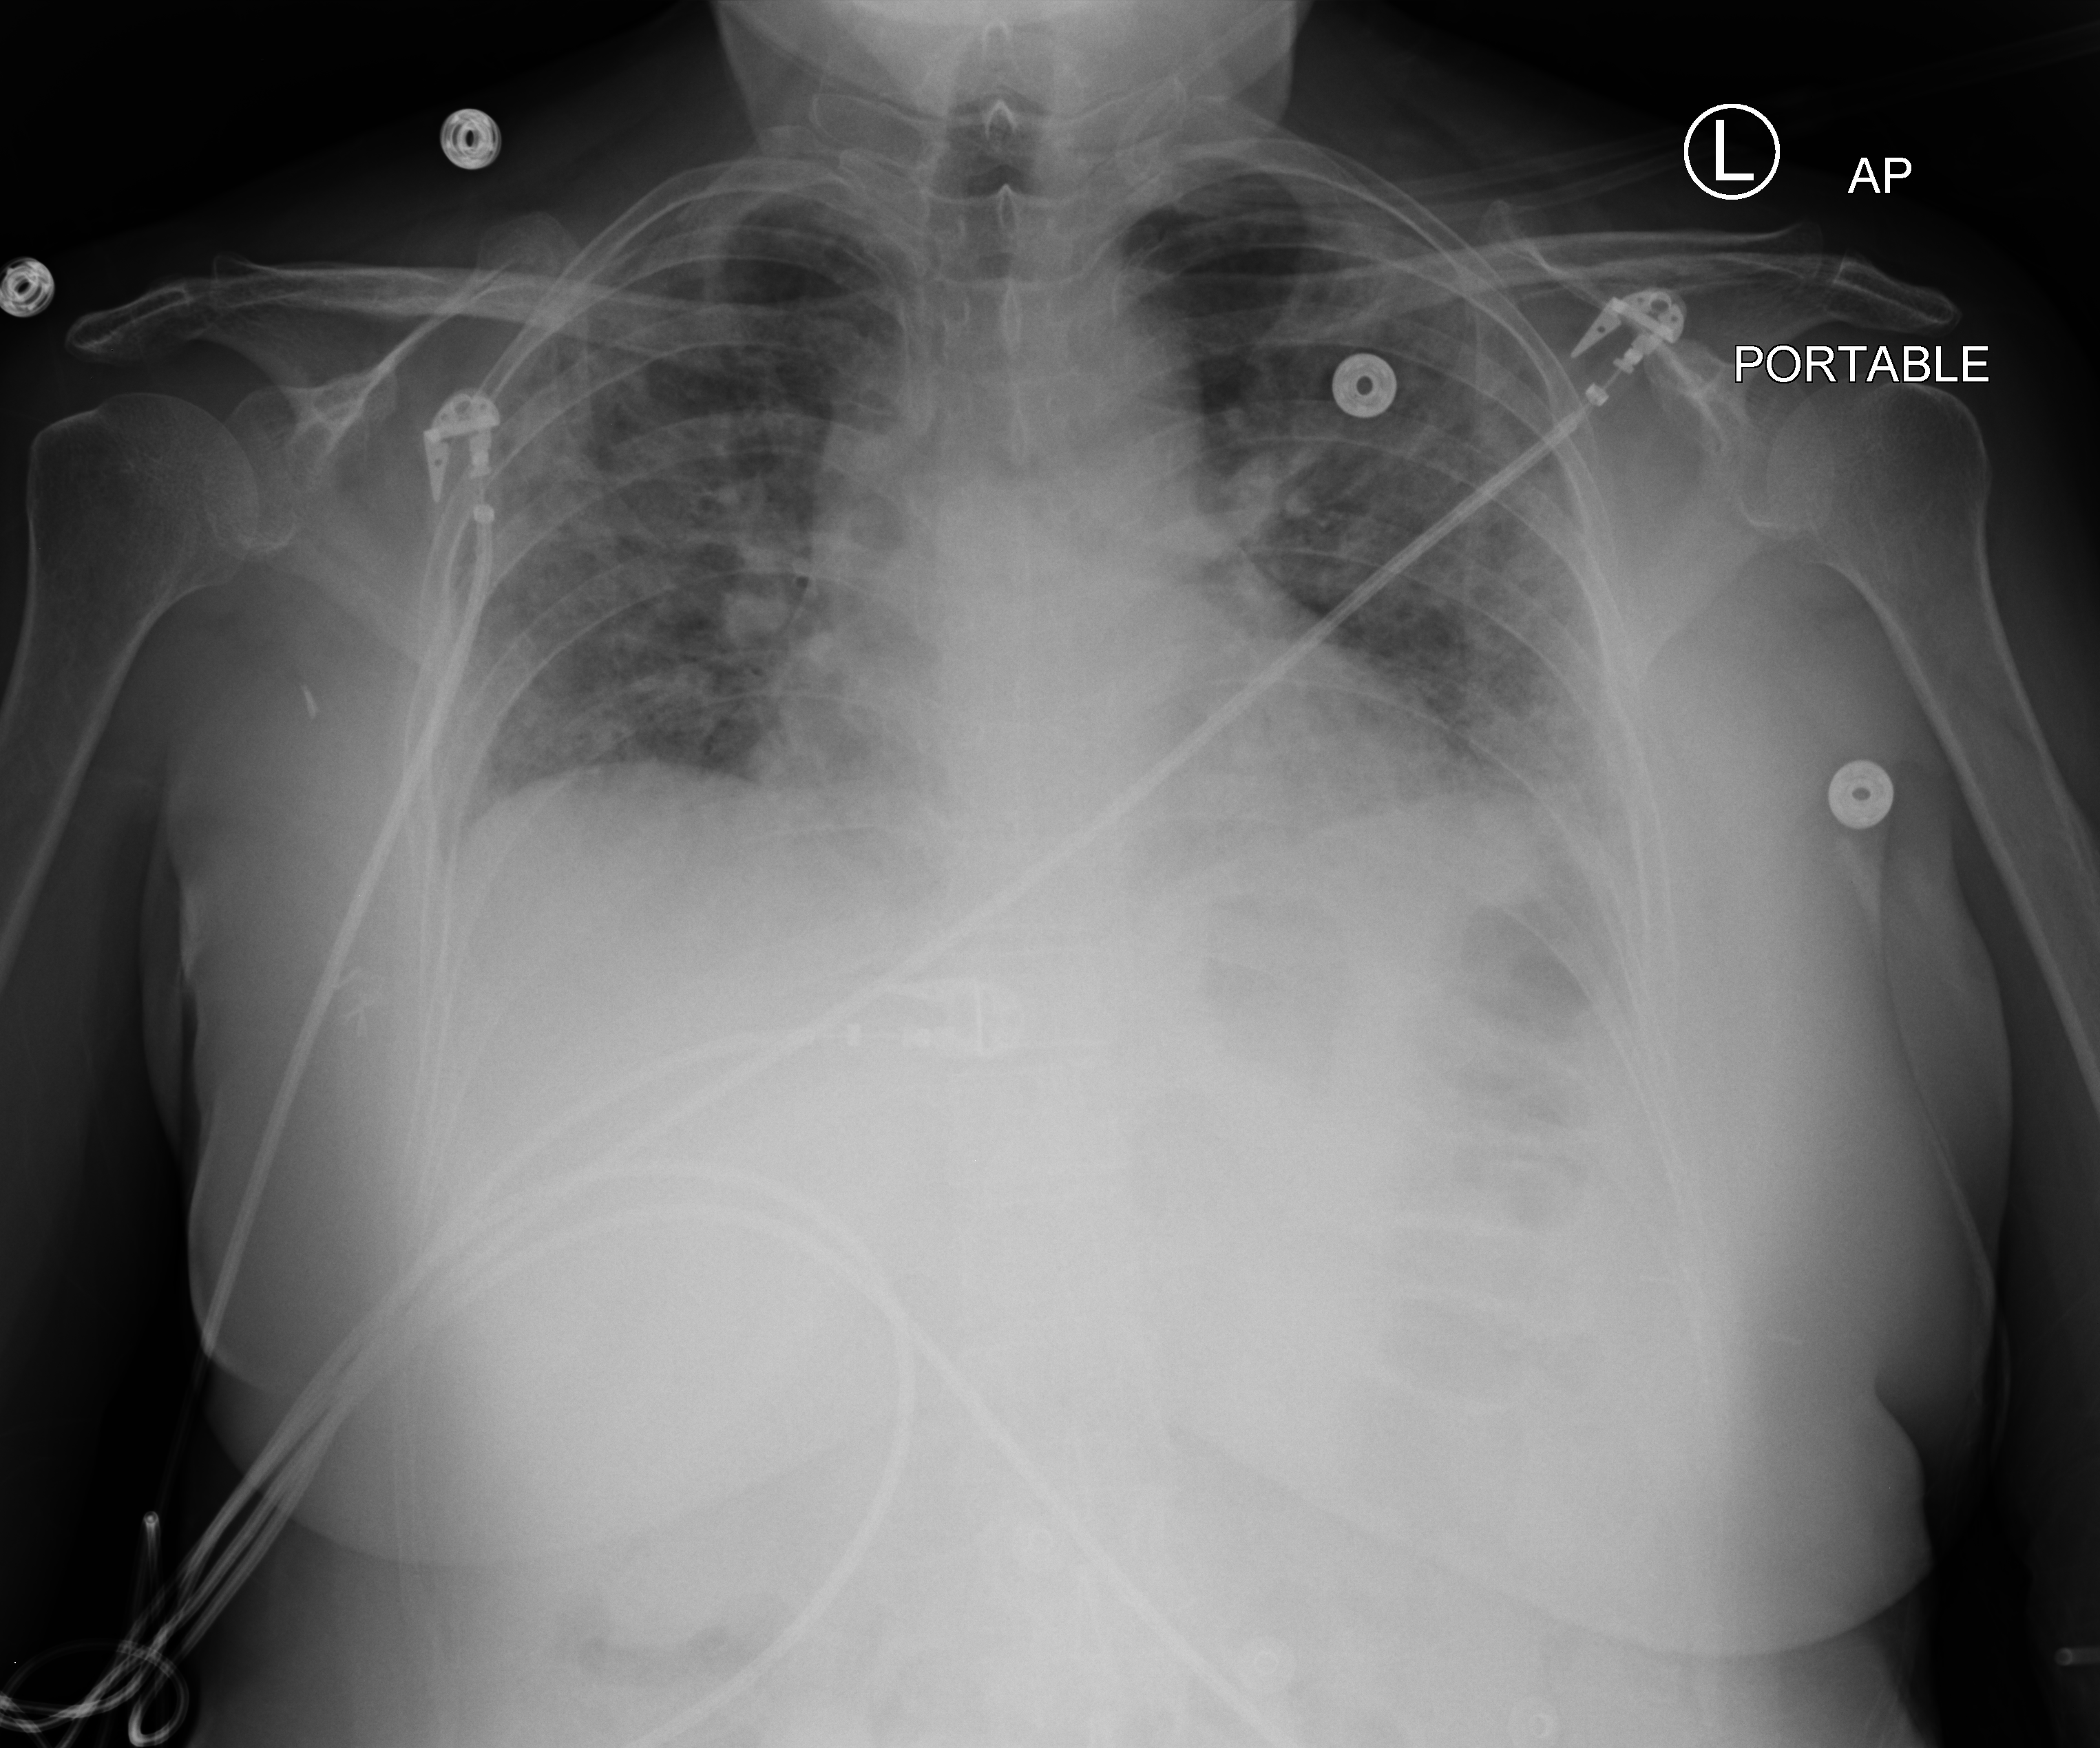
Chest X-ray (portable). Female patient hospitalised with COVID-19, age 18–59 years.
Hospital-stay facts (about this admission, not read from this image; timing relative to this image not recorded): smoking status (admission record): never; other chronic lung disease (admission record): no.